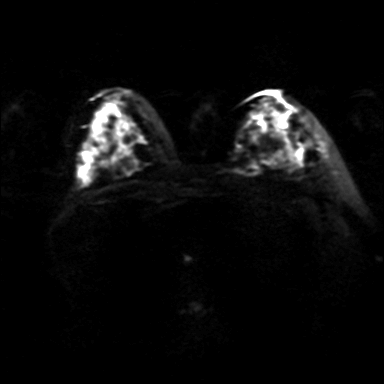
Breast MRI, one axial slice; position 22 of 36 along the scan axis; diffusion-weighted series; image 2 of 4 stored at this slice position (different b-values; order by instance number); 3 T; 4 mm slice thickness; 384 × 384 image matrix. Female patient.
Structures marked on this image (outlined manually by an expert reader):
- tumour on diffusion-weighted imaging: box from (x=255, y=112) to (x=292, y=144) px